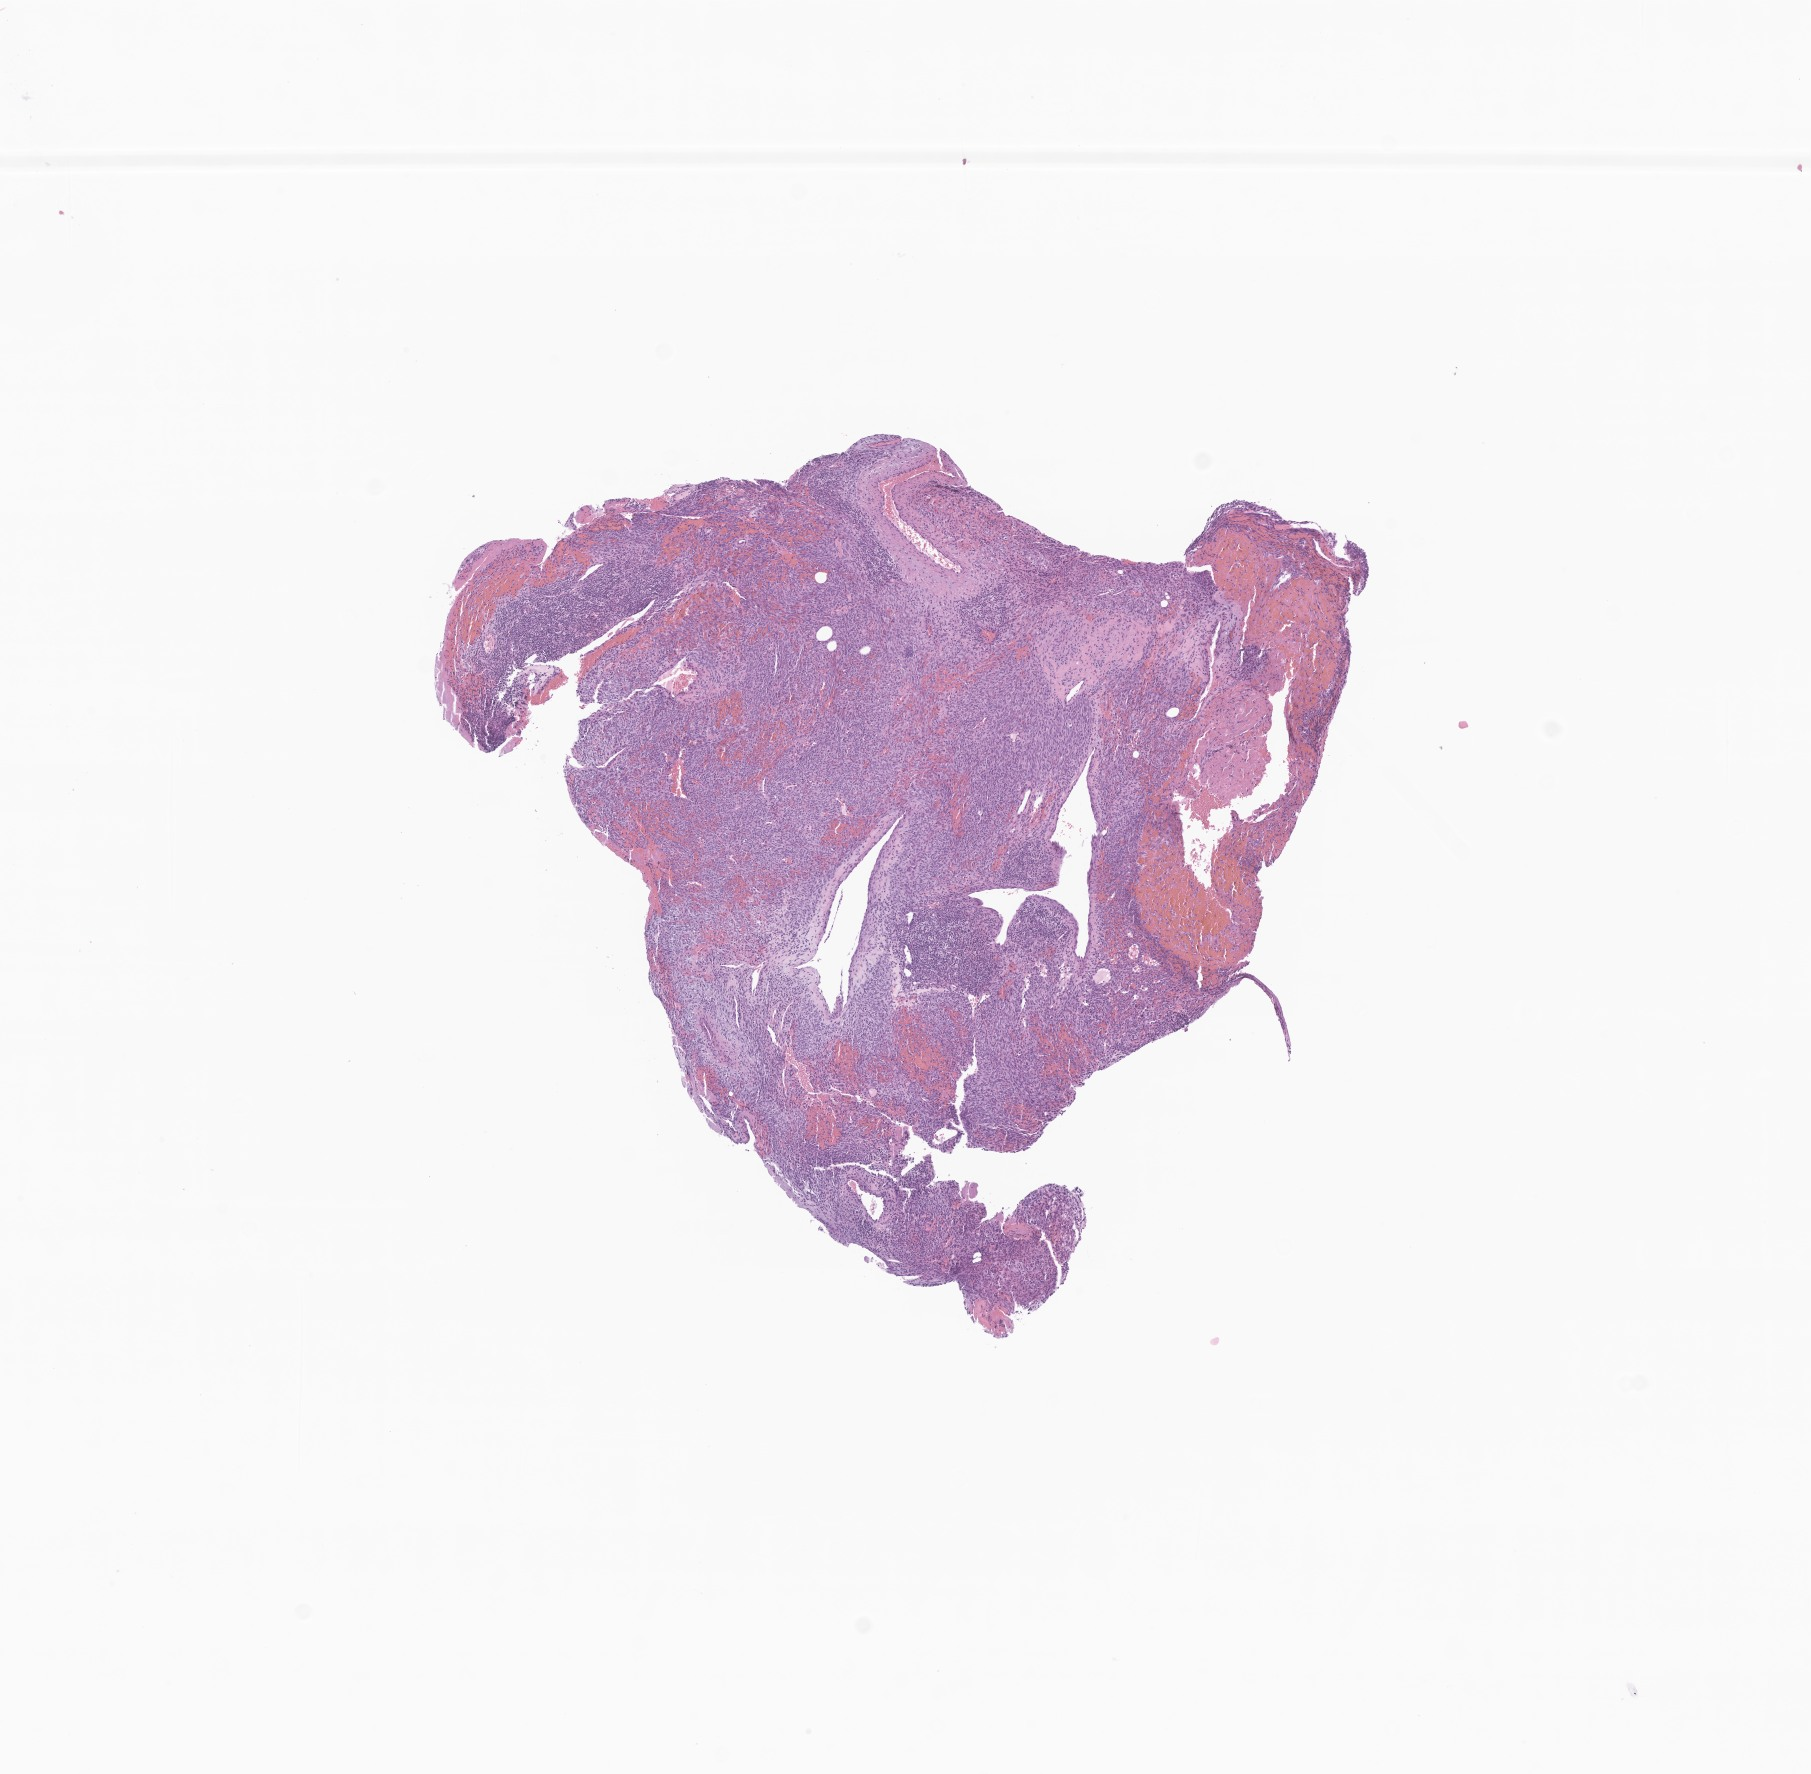
Digitized haematoxylin and eosin-stained section of tumor tissue from the mandible, low-resolution overview of the scanned area, about 7.6 x 7.5 mm; formalin-fixed paraffin-embedded section. Male patient, age 224 months (18 years 8 months).
Diagnosis (ICD-O-3 morphology term): Neoplasm, malignant, uncertain whether primary or metastatic.